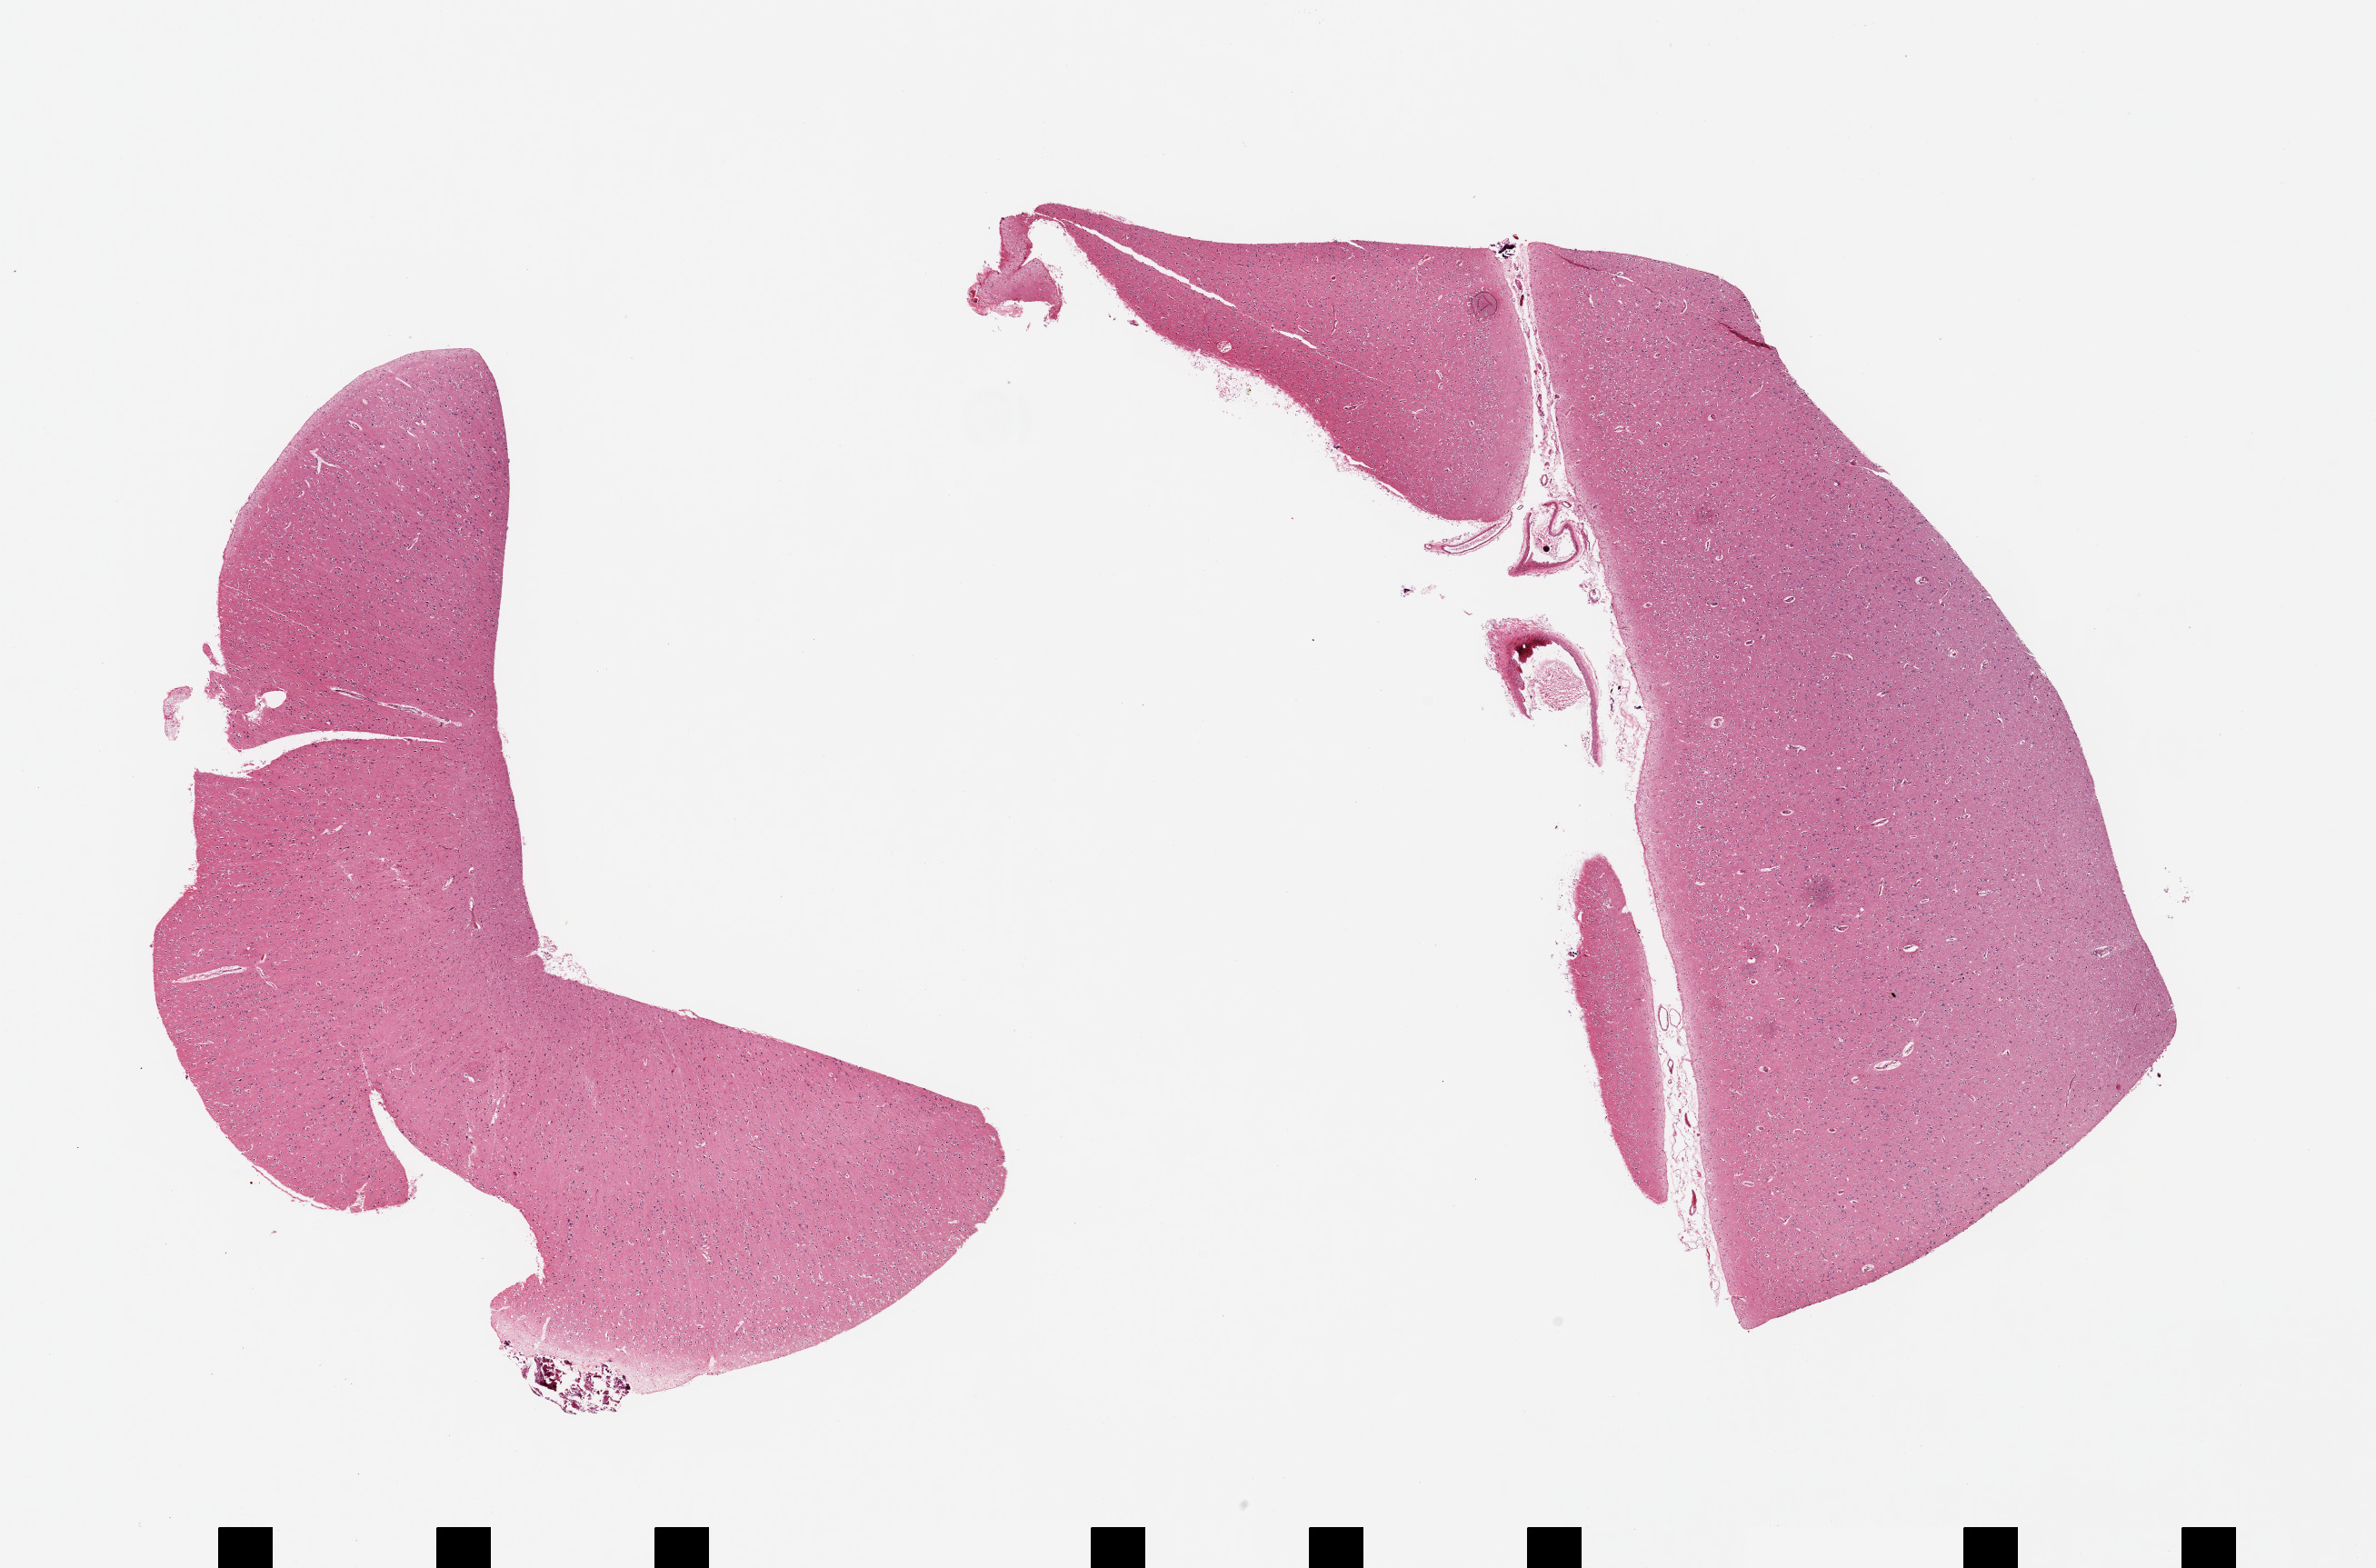
Digitized hematoxylin and eosin (H&E)-stained section, low-resolution overview of the scanned area, about 20.7 x 13.6 mm (slide scanned at 20x), PAXgene-fixed, paraffin-embedded tissue, sampled site (target tissue): cerebral cortex, tissue donor sample. Donor: female.
• reviewer comment on this tissue sample: 2 pieces; meningeal blood vessels included